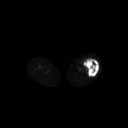
FDG PET of an extremity soft-tissue mass (from a PET/CT study), one axial slice. Slice 212 of 267 in the series (ordered by position). 3.27 mm slice thickness. 128 × 128 image matrix, field of view 700 × 700 mm. Patient: female, 62 years. Case-level facts recorded for this patient, not image findings: histological type: undifferentiated – high grade; grade: high; site of the primary tumour: left thigh.
Structures marked on this image (expert contour drawn on MRI and transferred to this co-registered scan by the dataset authors):
- gross tumour volume including surrounding oedema: bounding box [x1, y1, x2, y2] px = [83, 58, 99, 77]
- gross tumour volume (mass): [84, 59, 99, 77]